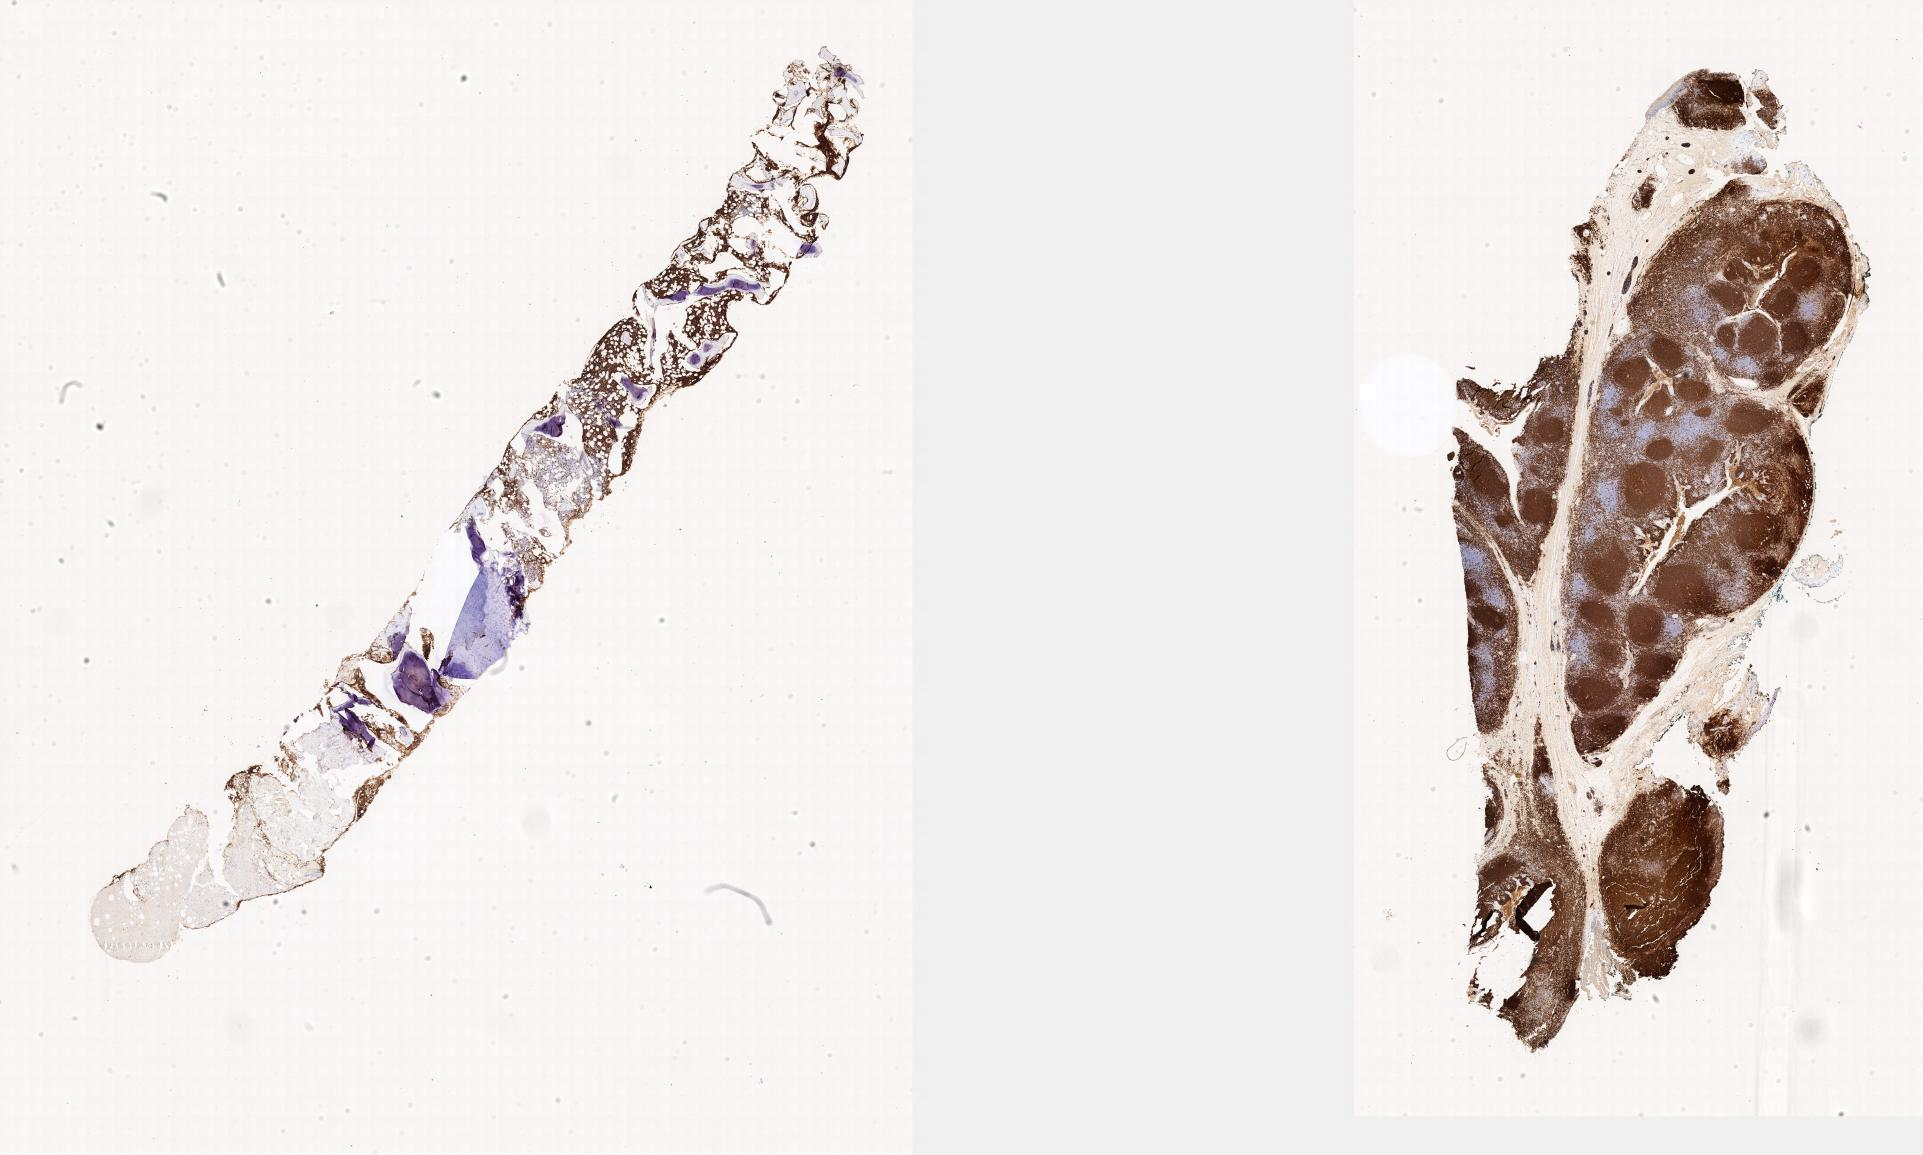
Immunohistochemistry (IHC) whole-slide image stained for CD20, whole scanned area shown as a low-resolution overview, tumor tissue, anatomic site: bone marrow. Male patient, aged 15.
Histologic diagnosis: Burkitt lymphoma, NOS.